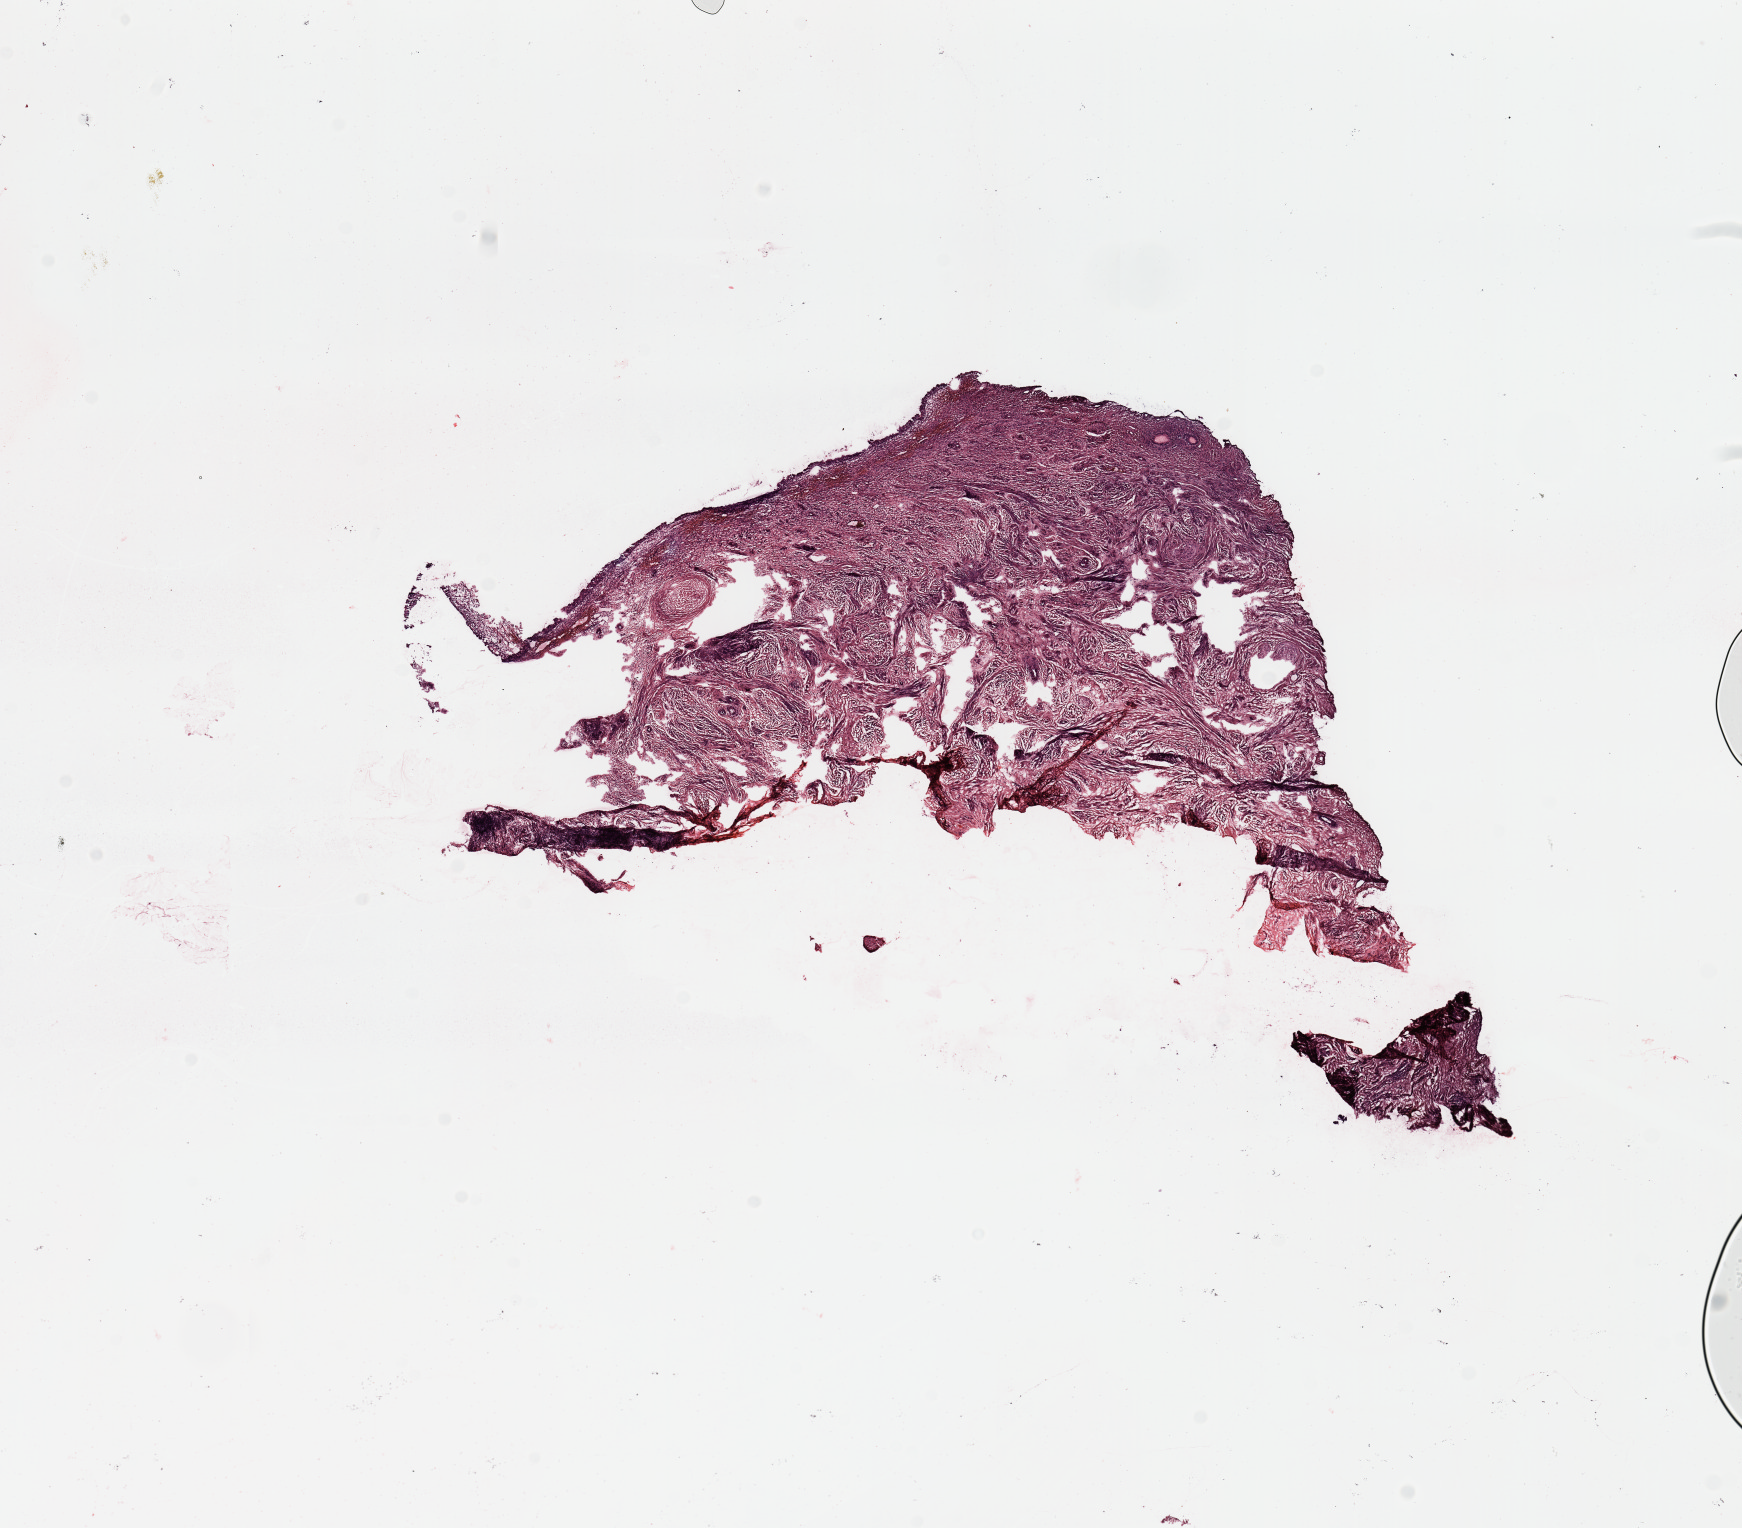
Whole-slide histology image, H&E — low-resolution overview of the scanned area, about 13.8 x 12.1 mm; uterus, normal (non-tumour) tissue. Female, 62 y/o.
This section: normal (non-tumour) tissue from the same patient. Patient diagnosis: Endometrioid adenocarcinoma, NOS.